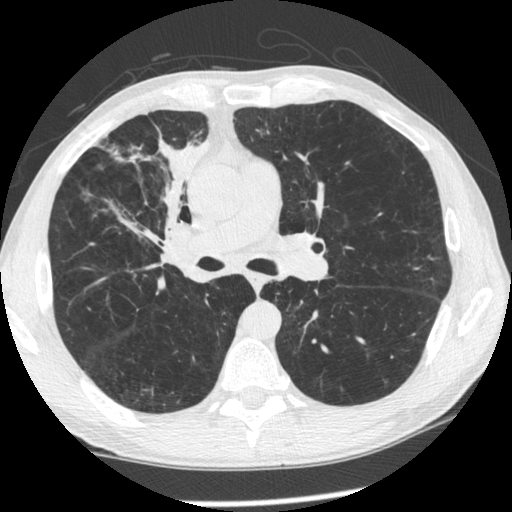
Low-dose screening chest CT, one axial slice; position 138 of 261 along the scan axis; 120 kVp; lung window (W 1500 / L -600 HU); 512 × 512 image matrix, field of view 340 × 340 mm.
Outlined on this slice (expert manual segmentation):
- lesion 1 (tumor, upper lobe of right lung): bounding box [x1, y1, x2, y2] px = [112, 138, 209, 236]